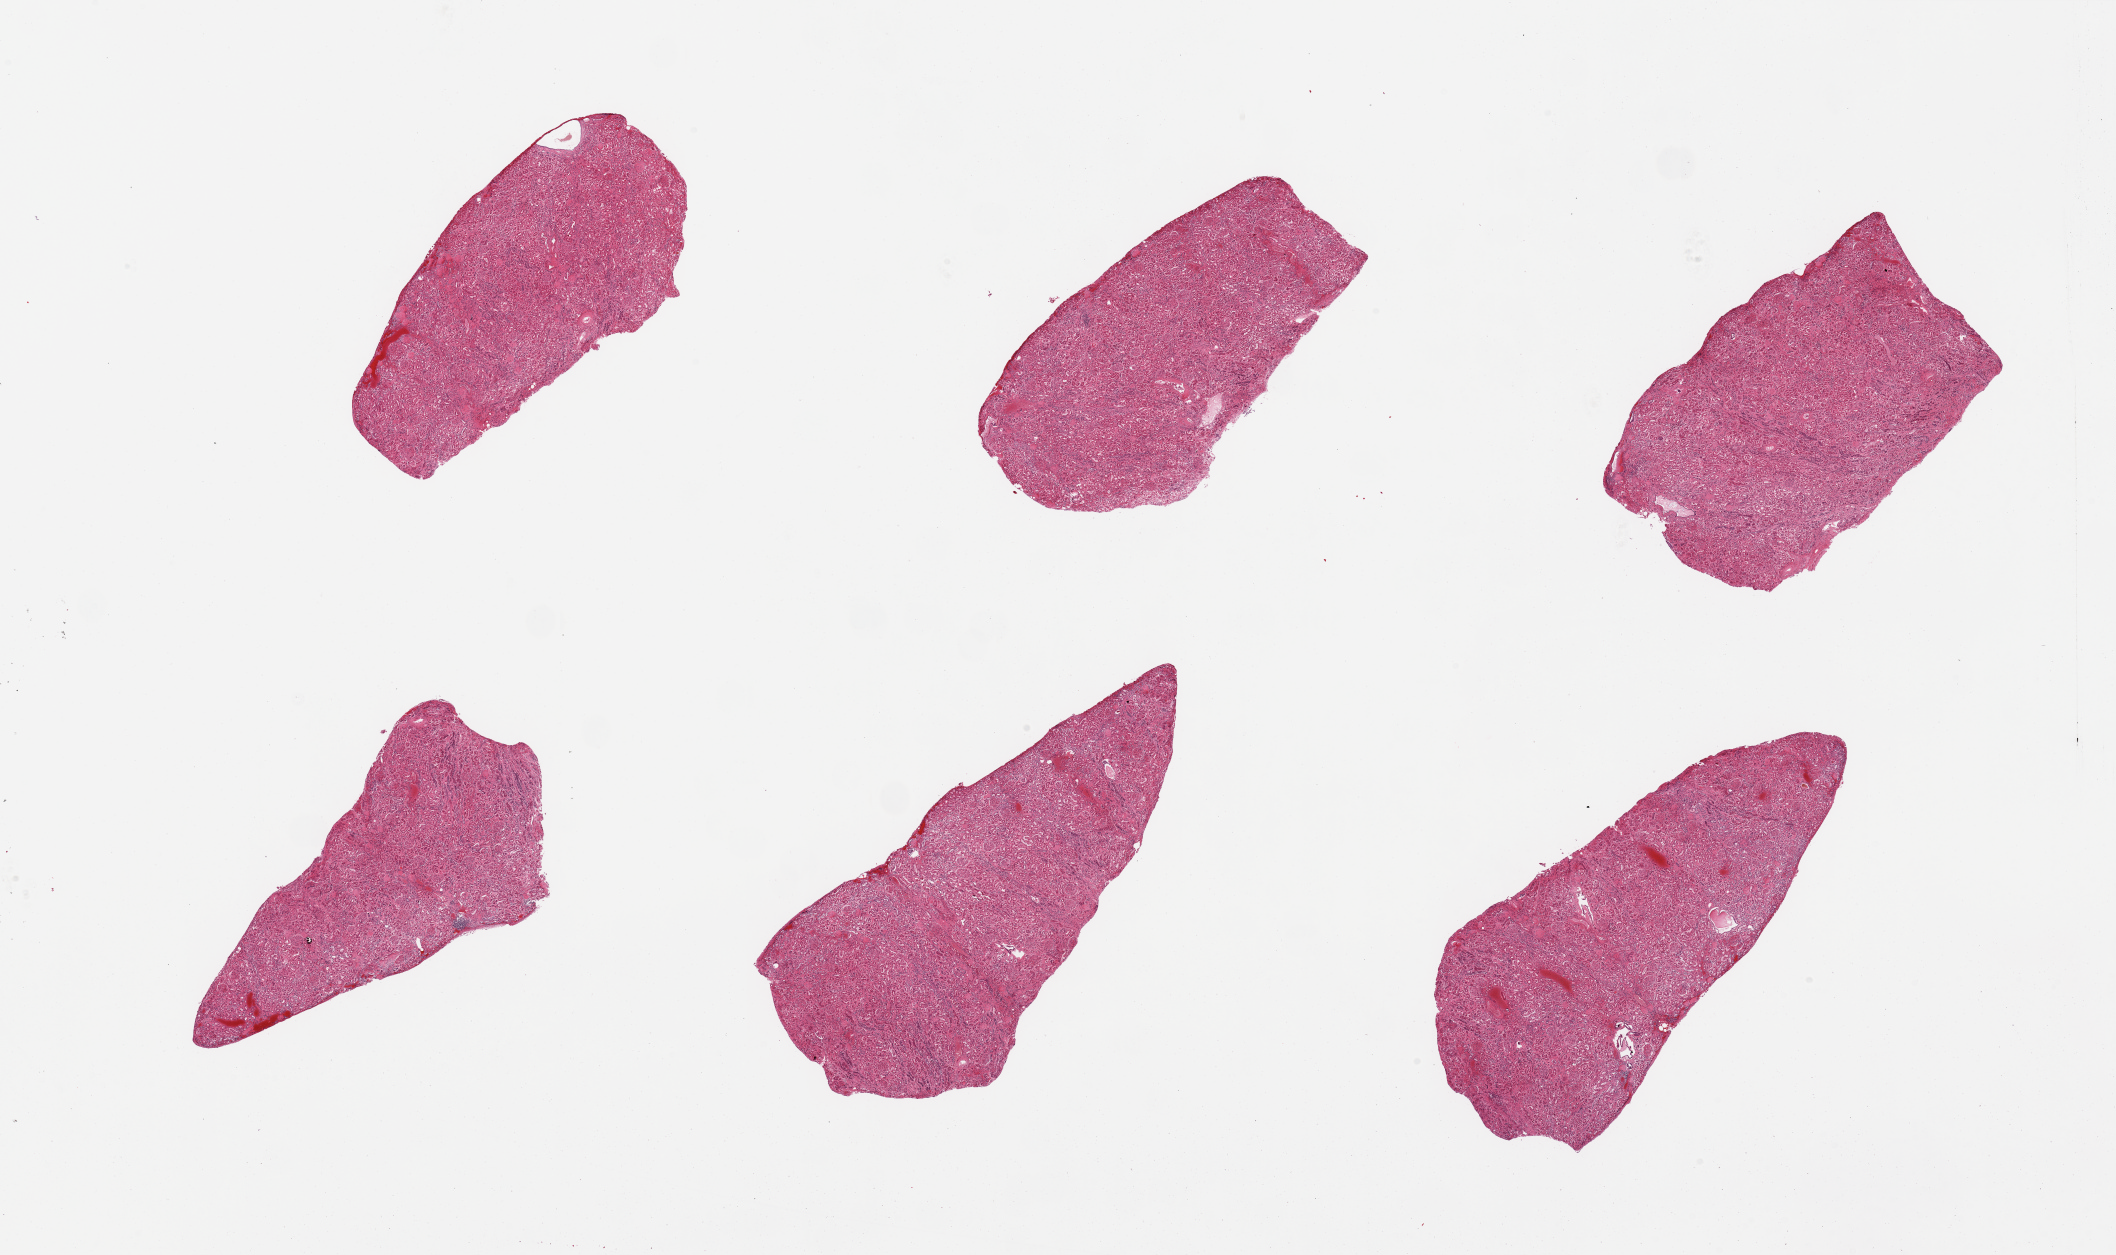
Digitized haematoxylin and eosin-stained section, brightfield — shown as a low-resolution overview of the whole scanned area (about 33.5 x 19.9 mm), PAXgene-fixed, paraffin-embedded tissue, target tissue: renal cortex, donor tissue sample.
Review note (as recorded): 6 pieces, all with glomeruli, badly autolyzed; background marked glomerular and interstitial sclerosis/fibrosis.